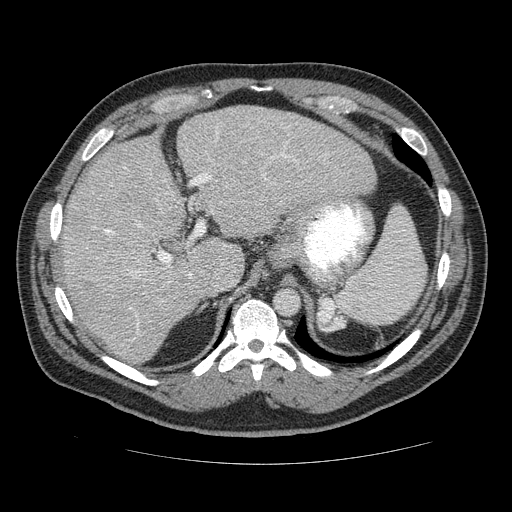
Contrast-enhanced abdominal CT (liver protocol), one axial slice; position 91 of 113 along the scan axis; 120 kVp; soft-tissue window (W 400 / L 40 HU); 2.5 mm slice thickness; 512 × 512 image matrix, field of view 400 × 400 mm. Case-level facts recorded for this patient, not image findings: diagnosis: hepatocellular carcinoma (patient treated with transarterial chemoembolisation; whether this scan precedes or follows treatment is not stated here); TNM stage (as recorded): Stage-II; Child-Pugh class: B.
Structures marked on this image (semi-automatically segmented with operator editing):
- liver parenchyma outside the tumour (the mass and vessels are separate outlines, so this box may not span the whole liver): box from (x=54, y=106) to (x=378, y=362) px
- mass: (x=102, y=250)–(x=175, y=301)
- liver vessels: (x=88, y=130)–(x=295, y=278)